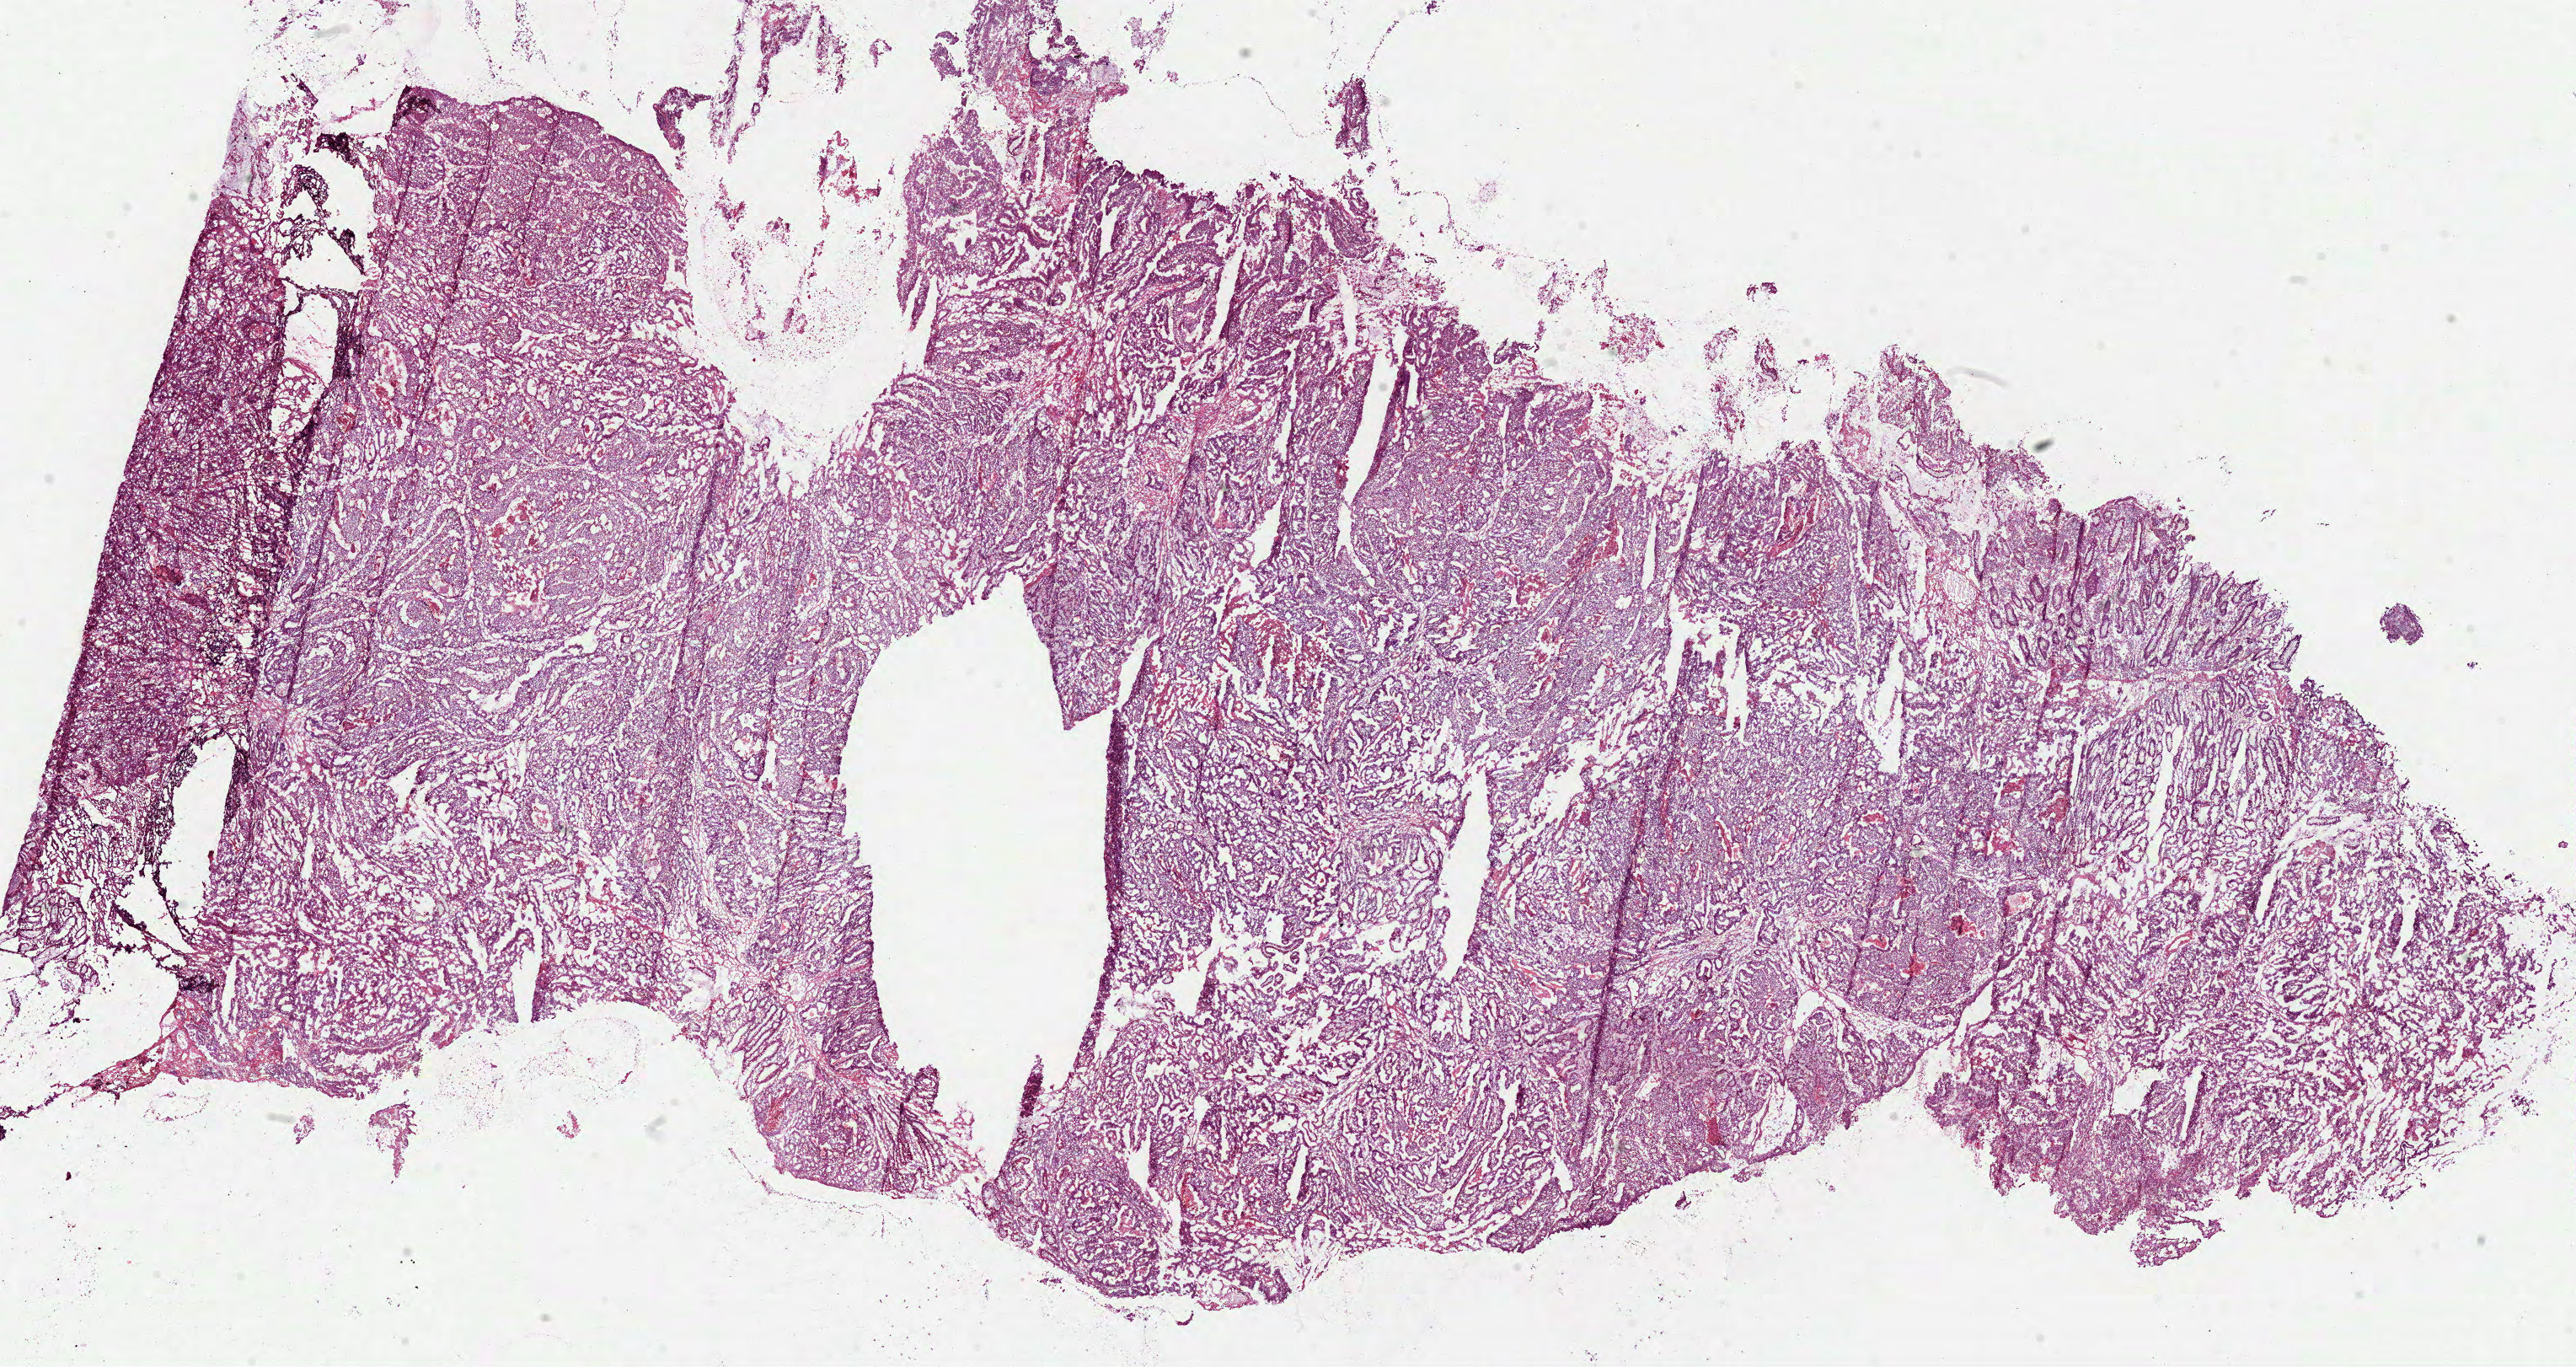
Digitized H&E tissue section (whole slide), low-resolution overview of the scanned area, about 24.7 x 13.1 mm (slide scanned at 40x), frozen section, sample: primary tumour, colon. Patient: male, age at initial diagnosis 81 years. Composition of this section per pathologist review: tumour cells 65%, tumour nuclei 80%, normal cells 15%, stromal cells 10%, necrosis 10%.
Histologic diagnosis: Adenocarcinoma, NOS (cecum). AJCC pathologic stage: IV (6th edition). Lymph nodes positive (case pathology): 10 of 17 examined.